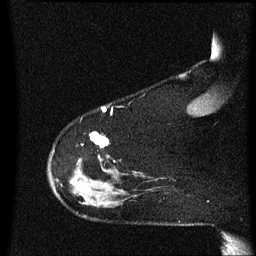
Breast MRI (dynamic contrast-enhanced), one sagittal slice. Position 51 of 60 along the scan axis. Dynamic contrast-enhanced series, image 2 of 3 at this slice position (ordered by acquisition). 1.5 T. TE 4.2 ms, TR 8.4 ms. 2 mm slice thickness. 256 × 256 image matrix, field of view 200 × 200 mm. Patient: female, 48 years.
Annotated regions visible in this slice (semi-automatically segmented with operator editing):
- analysis volume of interest (the breast-tissue region the enhancement analysis was run in; not a lesion): box from (x=49, y=134) to (x=126, y=217) px
- tumour enhancement mask (voxels above the 70 % enhancement threshold inside the analysis volume of interest): (x=71, y=134)–(x=109, y=185)